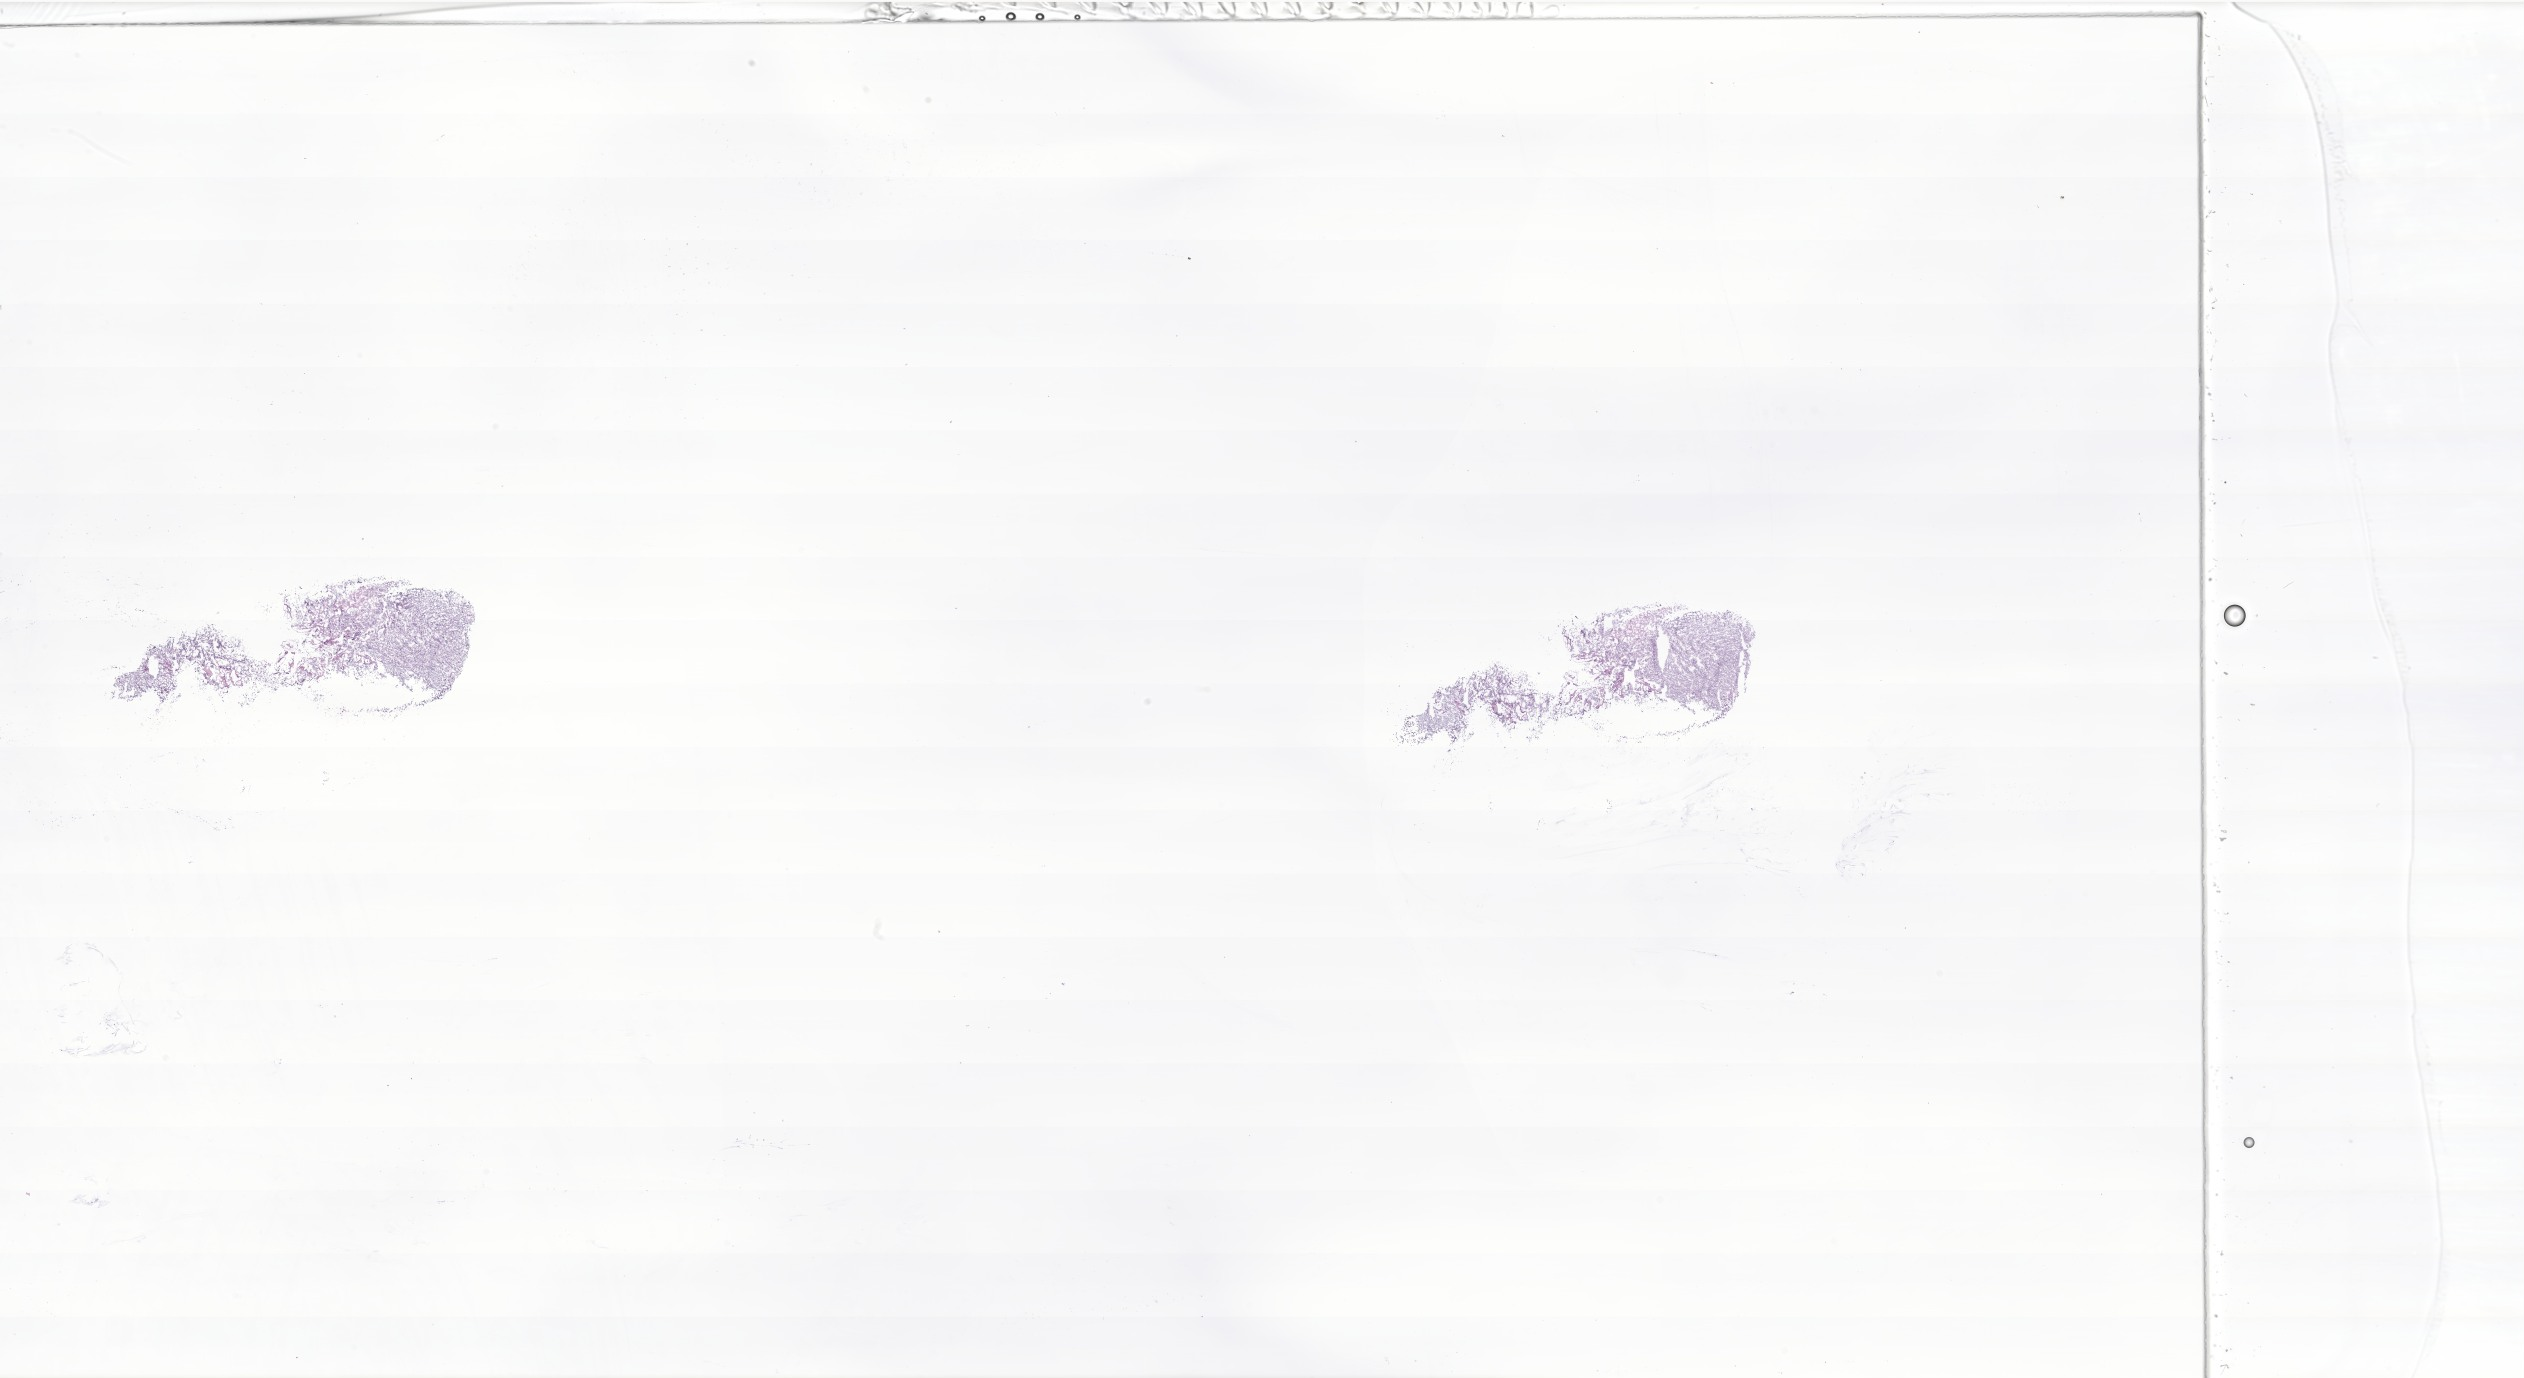
Digitized H&E-stained section of tumor tissue from the brain — whole scanned area (about 42.6 x 23.2 mm) shown as a low-resolution overview, cryosection (OCT / tissue freezing medium). Patient: male, age 82 months (6 years 10 months).
Recorded diagnosis: Neoplasm, malignant.